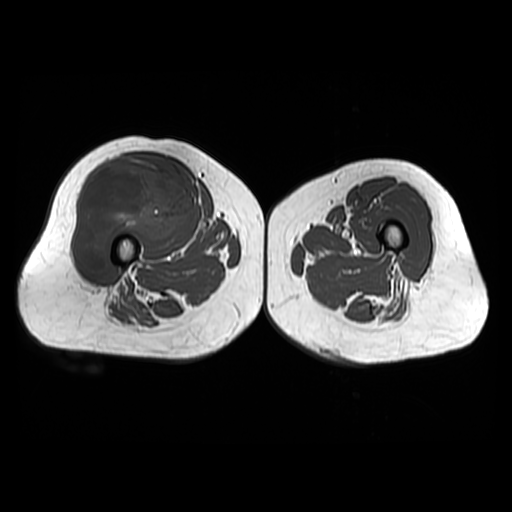
MRI of an extremity soft-tissue mass, one axial slice; position 29 of 48 along the scan axis; 512 × 512 image matrix, field of view 440 × 440 mm. Female patient. From the clinical record (not read from this slice): histological type: pleiomorphic undifferentiated sarcoma; grade: high; site of the primary tumour: right quadricep.
Structures marked on this image (expert manual segmentation):
- gross tumour volume including surrounding oedema: bounding box [x1, y1, x2, y2] px = [73, 156, 197, 275]
- gross tumour volume (mass): [73, 156, 197, 275]